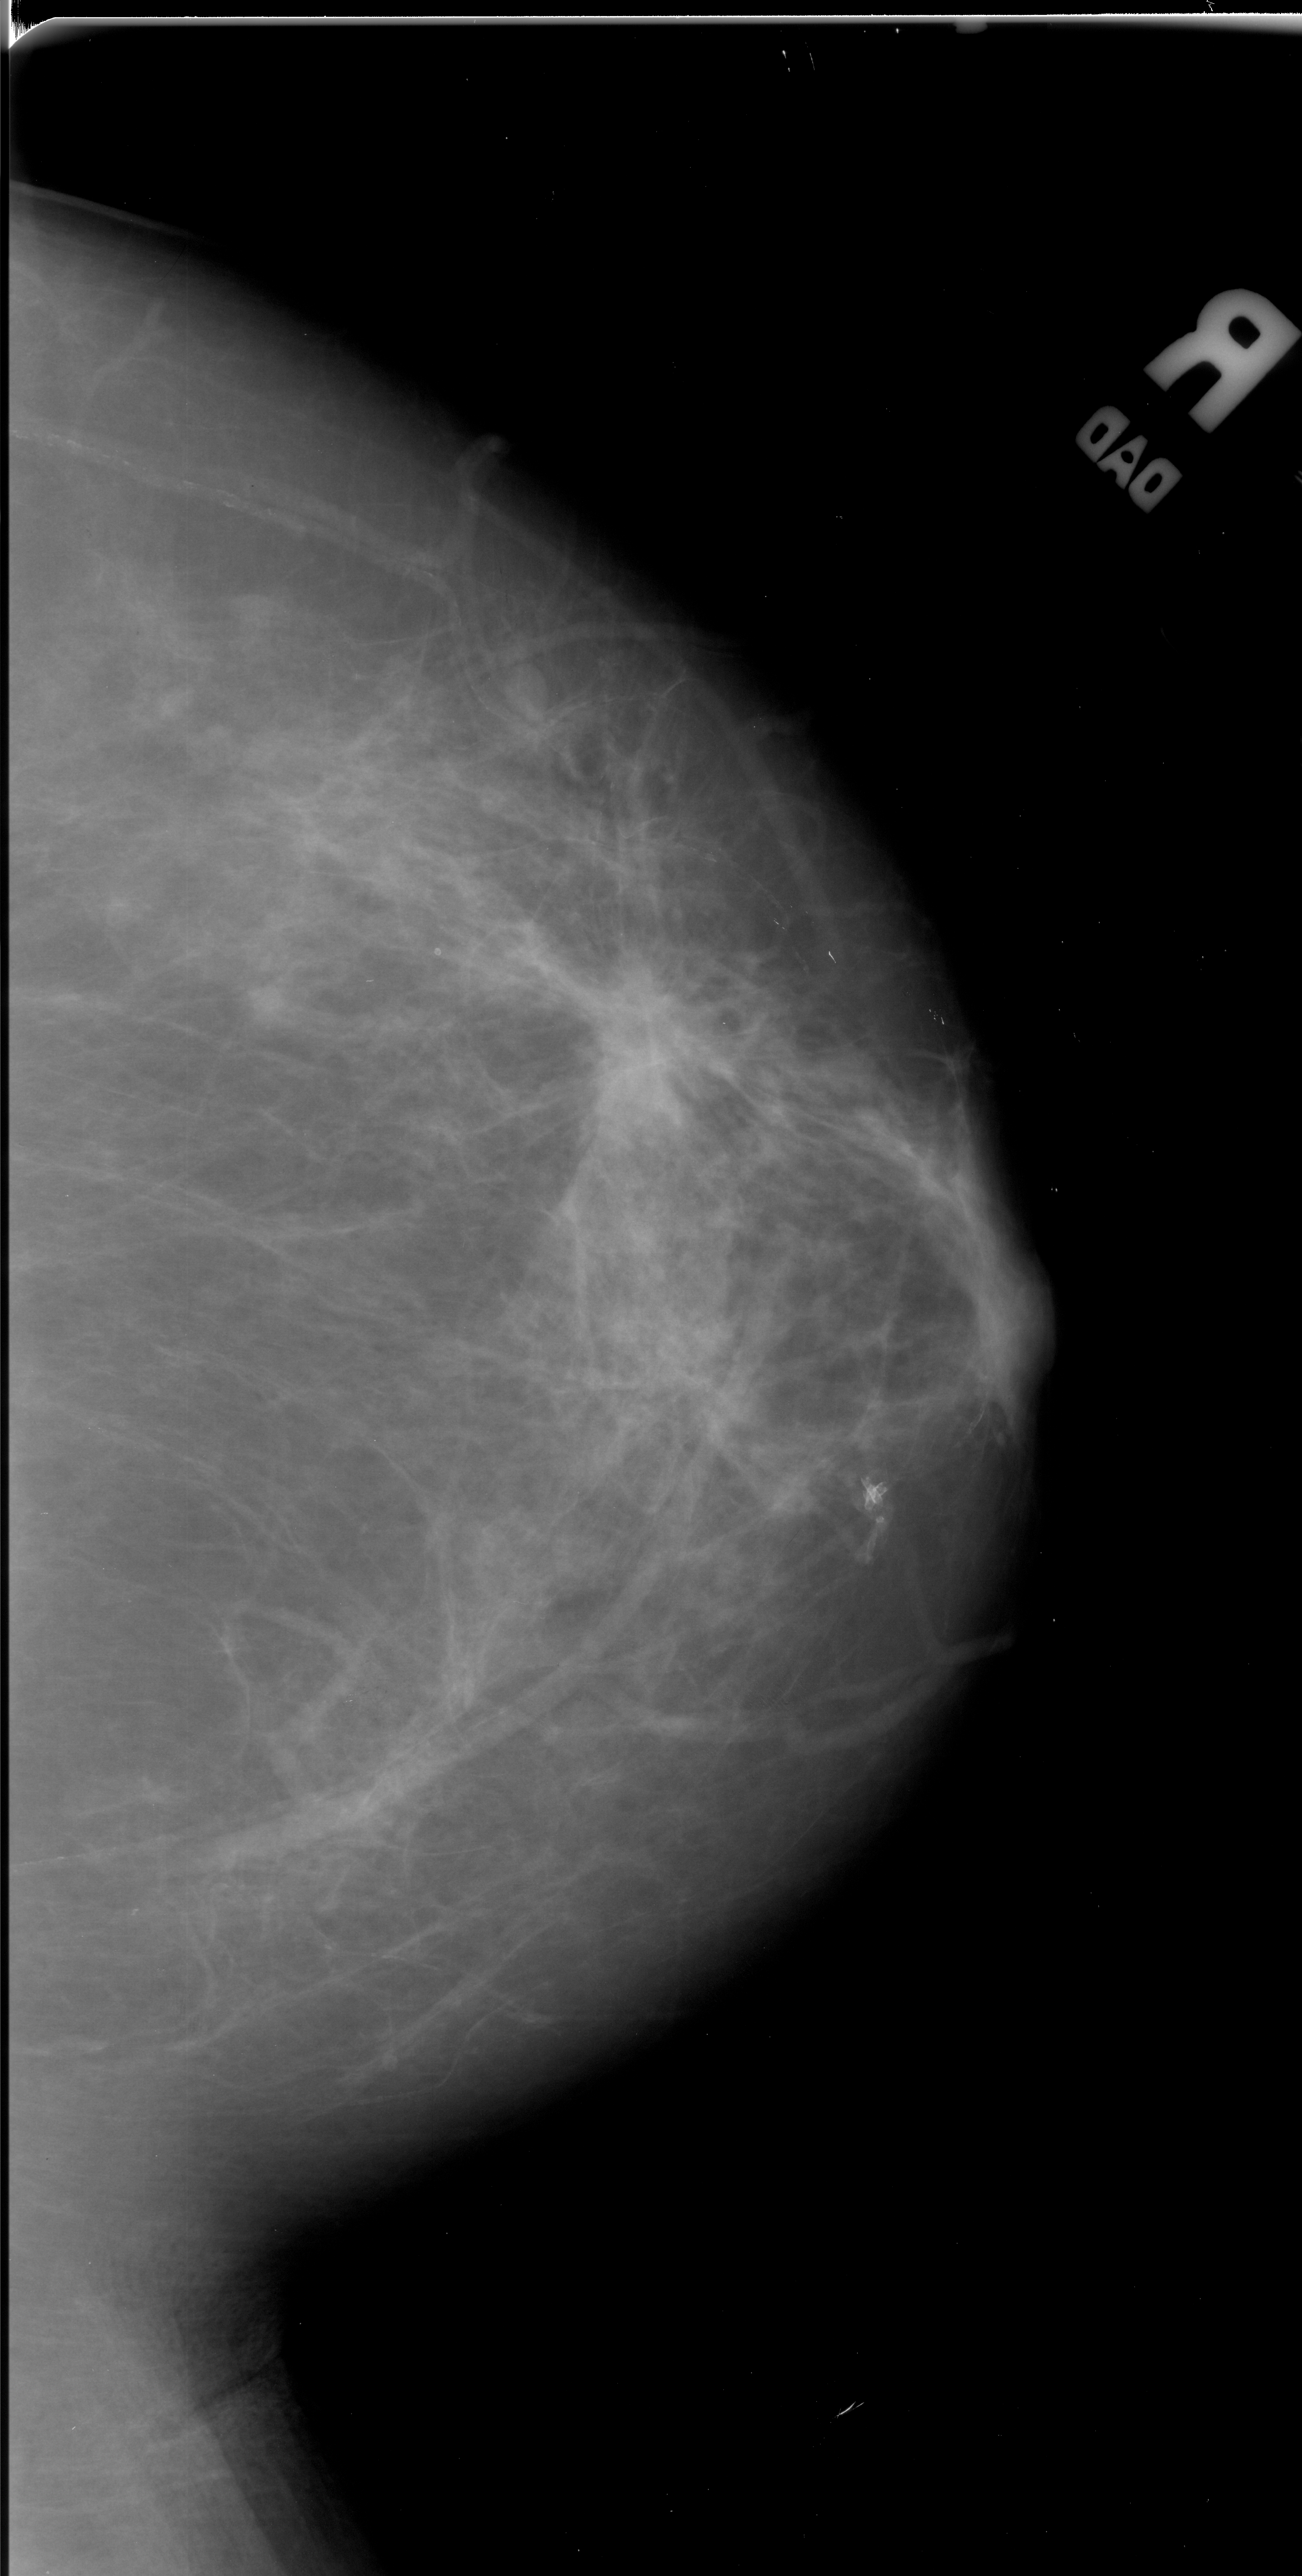
Digitized screen-film mammogram; right breast; craniocaudal (CC) view; breast composition: scattered fibroglandular densities (BI-RADS density category 2 of 4).
- Marked abnormality: mass, shape irregular, margins spiculated; BI-RADS assessment category 5; pathology result (as recorded, not read from the image): malignant.